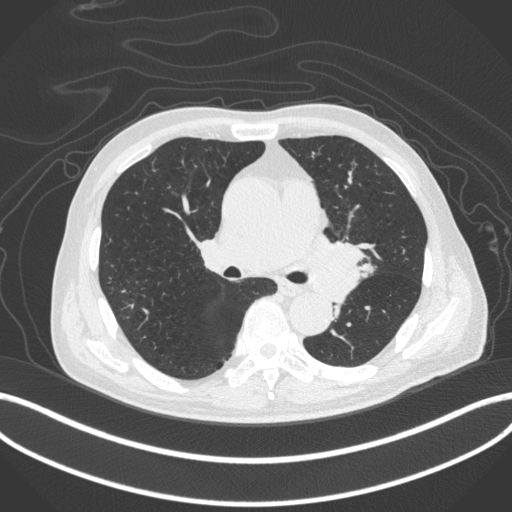
Chest CT, one axial slice; slice 253 of 420 in the series (ordered by position); reconstruction kernel B31f; 120 kVp; lung window (W 1500 / L -600 HU); 1 mm slice thickness; 512 × 512 image matrix. Male patient, age 77 years. From the clinical record (not read from this slice): clinical TNM (as recorded): T3 N1 M0.
Annotated regions visible in this slice (bounding box drawn by a radiologist):
- lung tumour (recorded histology: adenocarcinoma): box from (x=306, y=236) to (x=375, y=307) px